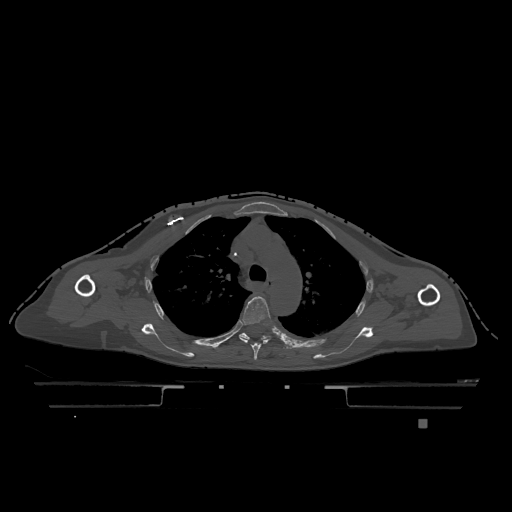
CT including the spine, one axial slice. Position 866 of 1317 along the scan axis. Bone window (W 1800 / L 400 HU). 512 × 512 image matrix. Female patient, age 74 years. Case-level facts recorded for this patient, not image findings: primary cancer: lung; vertebrae with lytic lesions (as recorded): T1, T4, T5, T6, L4, L5.
Structures marked on this image (semi-automatic segmentation, software-assisted and operator-edited):
- T4 vertebra: bounding box (x1, y1, x2, y2) in pixels: (239, 296, 272, 360)
- T5 vertebra: (239, 333, 268, 340)